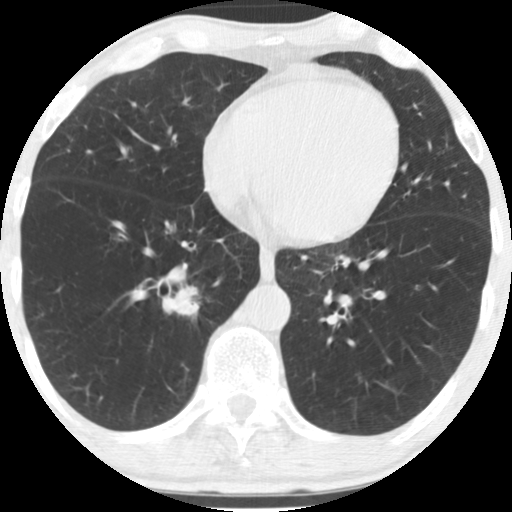
Chest CT (low-dose screening protocol), one axial image, first (baseline) screen, lung window (W 1500 / L -600 HU), standard (soft-tissue) reconstruction kernel (STANDARD), 120 kVp, slice 114 of 170 in the series, 512 × 512 image matrix, field of view 290 × 290 mm. Male, age 67 years at enrolment. Former smoker at enrolment.
• Expert reader's lesion annotation, bounding box <154,272,216,331> (left, top, right, bottom; pixels).
• The exam's reader record, not a measurement of the box and not confirmed to be the same lesion: non-calcified nodule or mass ≥4 mm, right lower lobe, 16 × 16 mm, spiculated (stellate) margins, soft tissue attenuation.
• Official screen result: positive, change unspecified: nodule(s) >= 4 mm or enlarging nodule(s), mass(es), or other non-specific abnormalities suspicious for lung cancer.